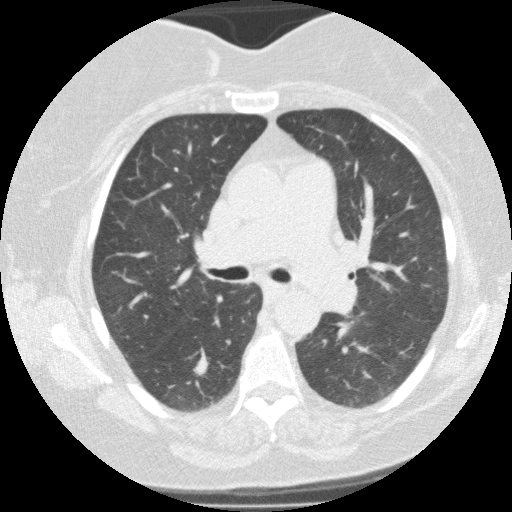
Low-dose screening chest CT, one axial slice. Position 89 of 146 along the scan axis. 120 kVp. Lung window (W 1500 / L -600 HU). 2 mm slice thickness. 512 × 512 image matrix.
Outlined on this slice (outlined manually by an expert reader):
- lesion 3 (nodule, lower lobe of right lung): box from (x=193, y=360) to (x=209, y=377) px